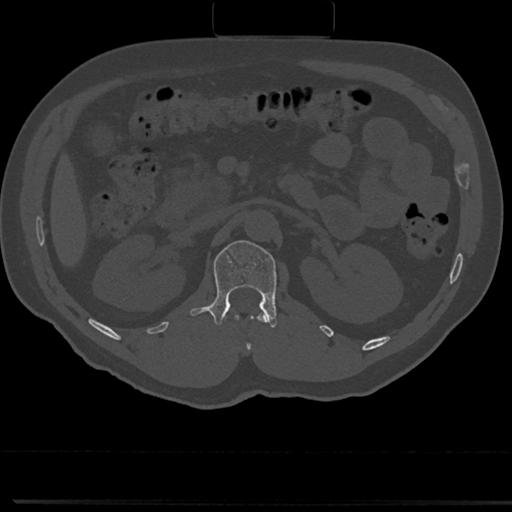
CT including the spine, one axial slice; slice 97 of 817 in the series (ordered by position); reconstruction kernel Br40s/3; bone window (W 1800 / L 400 HU); 0.5 mm slice thickness; 512 × 512 image matrix. Male patient, age 61 years. Case-level facts recorded for this patient, not image findings: primary cancer: prostate.
Annotated regions visible in this slice (semi-automatically segmented with operator editing):
- L1 vertebra: box from (x=191, y=240) to (x=278, y=327) px
- T12 vertebra: (x=248, y=314)–(x=266, y=347)